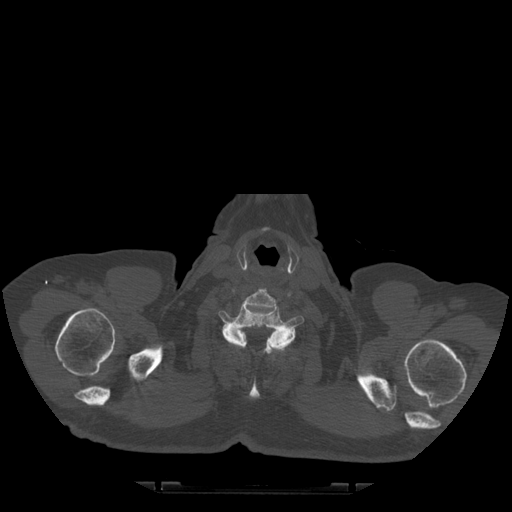
CT including the spine, one axial slice. Position 451 of 522 along the scan axis. Bone window (W 1800 / L 400 HU). 1.25 mm slice thickness. 512 × 512 image matrix. Patient age 72 years. From the clinical record (not read from this slice): primary cancer: prostate.
Annotated regions visible in this slice (semi-automatic segmentation, software-assisted and operator-edited):
- T1 vertebra: bounding box (x1, y1, x2, y2) in pixels: (231, 328, 293, 398)